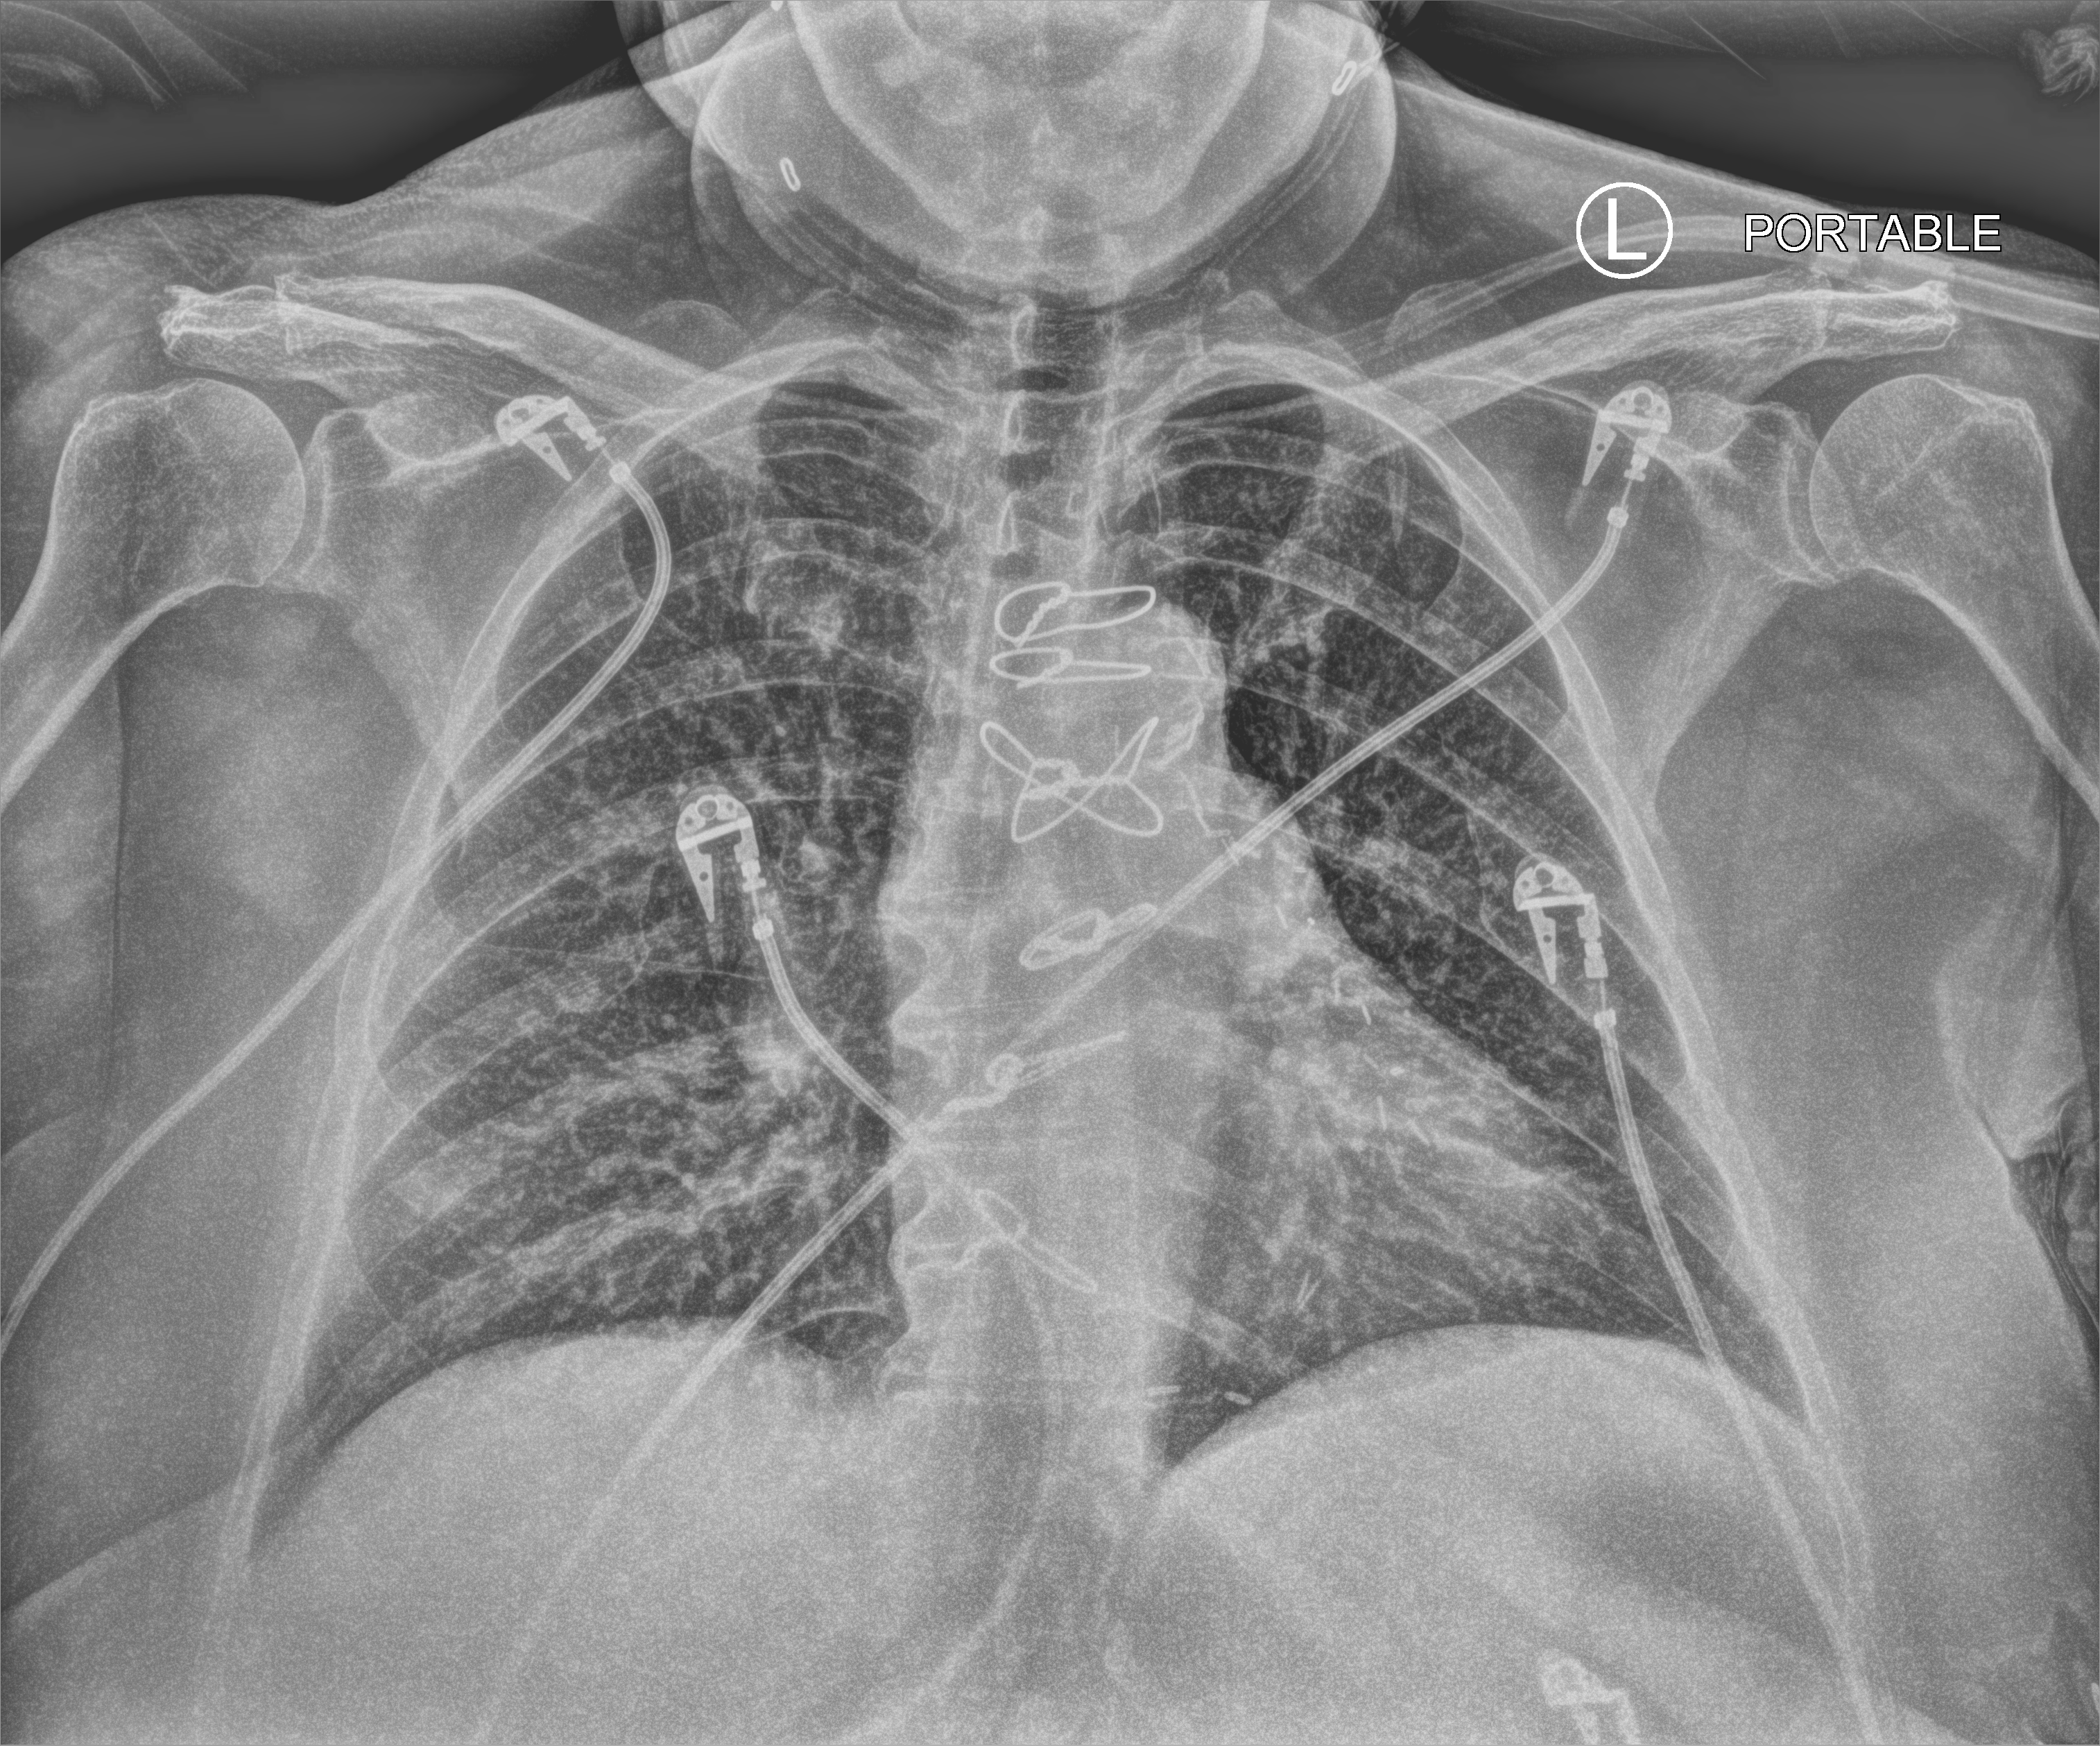
Bedside chest radiograph (computed radiography), anteroposterior (AP) projection. Female patient hospitalised with COVID-19, age 60–74 years.
Admission-level facts for this patient (not findings on this image; timing relative to this image not recorded):
- other chronic lung disease (admission record): no
- length of hospital stay: 13 days